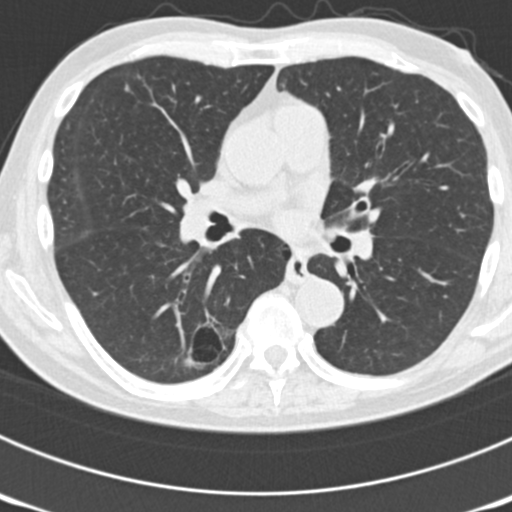
Axial slice from a low-dose chest CT screening exam, third screening round (two years after baseline), lung window (W 1500 / L -600 HU), 2 mm slice thickness, slice 77 of 177 in the series, 512 × 512 image matrix, field of view 300 × 300 mm. Male, age 70 years at enrolment. Current smoker at enrolment.
Lesion marked by an expert reader, bounding box (x1, y1, x2, y2) in pixels: (146, 305, 237, 385). The screening reader recorded 3 non-calcified nodules or masses ≥4 mm on this exam (right upper lobe, left upper lobe, right lower lobe); which of them this box marks is not recorded. Participant outcome: lung cancer diagnosed 14 days after this screen — bronchiolo-alveolar adenocarcinoma, NOS, right lower lobe, poorly differentiated (G3), stage IB (AJCC 6th edition), 30 mm at pathology.